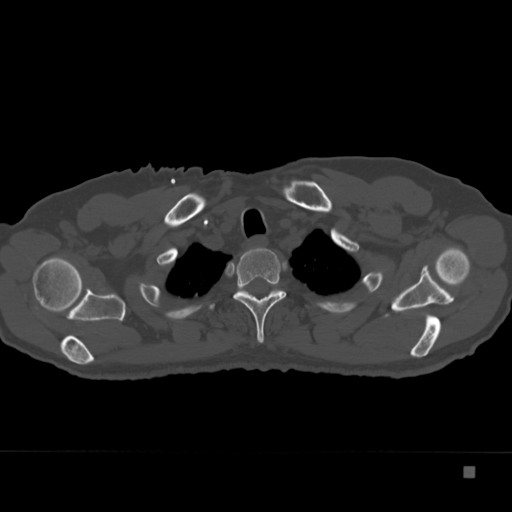
CT including the spine, one axial slice. Position 300 of 332 along the scan axis. Reconstruction kernel Br40s. 120 kVp. Bone window (W 1800 / L 400 HU). 1.5 mm slice thickness. 512 × 512 image matrix, field of view 389 × 389 mm. Patient: male, 72 years. From the clinical record (not read from this slice): primary cancer: skeletal.
Annotated regions visible in this slice (semi-automatically segmented with operator editing):
- T2 vertebra: bounding box (x1, y1, x2, y2) in pixels: (233, 247, 286, 343)
- T3 vertebra: (236, 283, 285, 297)